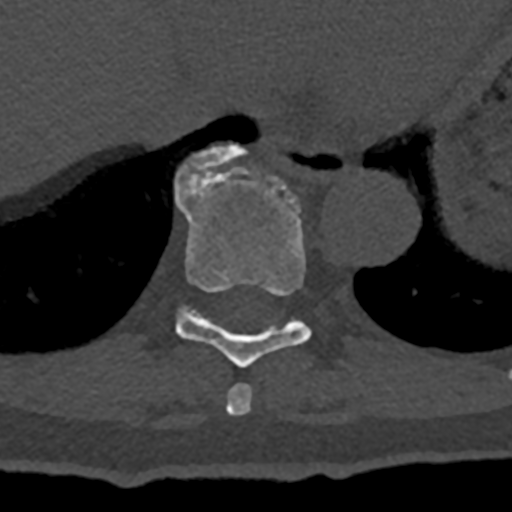
CT including the spine, one axial slice; position 648 of 797 along the scan axis; 120 kVp; bone window (W 1800 / L 400 HU); 0.5 mm slice thickness; 512 × 512 image matrix, field of view 160 × 160 mm. Patient: male, 74 years. From the clinical record (not read from this slice): primary cancer: renal; vertebrae with lytic lesions (as recorded): T10, L1, L2, L3, L4, L5.
Structures marked on this image (semi-automatically segmented with operator editing):
- T10 vertebra: bounding box [x1, y1, x2, y2] px = [175, 145, 247, 201]
- T8 vertebra: [226, 383, 252, 415]
- T9 vertebra: [175, 167, 312, 368]